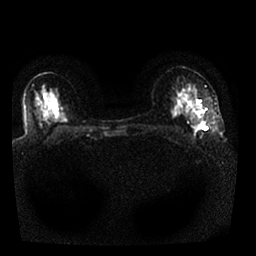
Breast MRI, one axial slice. Slice 15 of 25 in the series (ordered by position). Diffusion-weighted series; image 2 of 4 stored at this slice position (different b-values; order by instance number). 1.5 T. 256 × 256 image matrix, field of view 330 × 330 mm. Female patient.
Outlined on this slice (expert manual segmentation):
- tumour on diffusion-weighted imaging: bounding box [x1, y1, x2, y2] px = [195, 122, 205, 130]